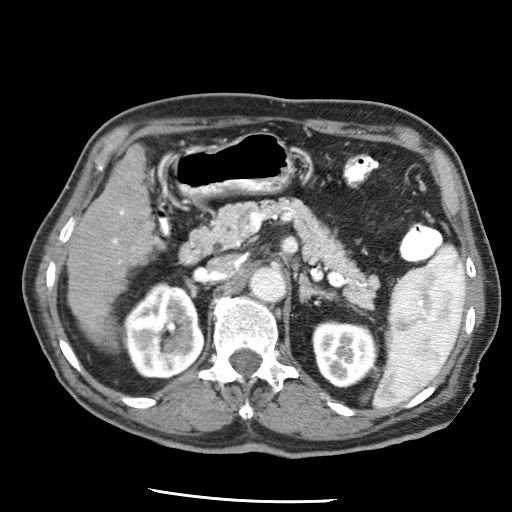
Contrast-enhanced abdominal CT (liver protocol), one axial slice. Position 20 of 79 along the scan axis. 120 kVp. Soft-tissue window (W 400 / L 40 HU). 2.5 mm slice thickness. 512 × 512 image matrix. From the clinical record (not read from this slice): diagnosis: hepatocellular carcinoma (patient treated with transarterial chemoembolisation; whether this scan precedes or follows treatment is not stated here); TNM stage (as recorded): Stage-IIIA; Child-Pugh class: A; tumour differentiation: moderately differentiated.
Annotated regions visible in this slice (semi-automatic segmentation, software-assisted and operator-edited):
- liver parenchyma outside the tumour (the mass and vessels are separate outlines, so this box may not span the whole liver): box from (x=67, y=146) to (x=154, y=336) px
- liver vessels: (x=112, y=209)–(x=135, y=263)